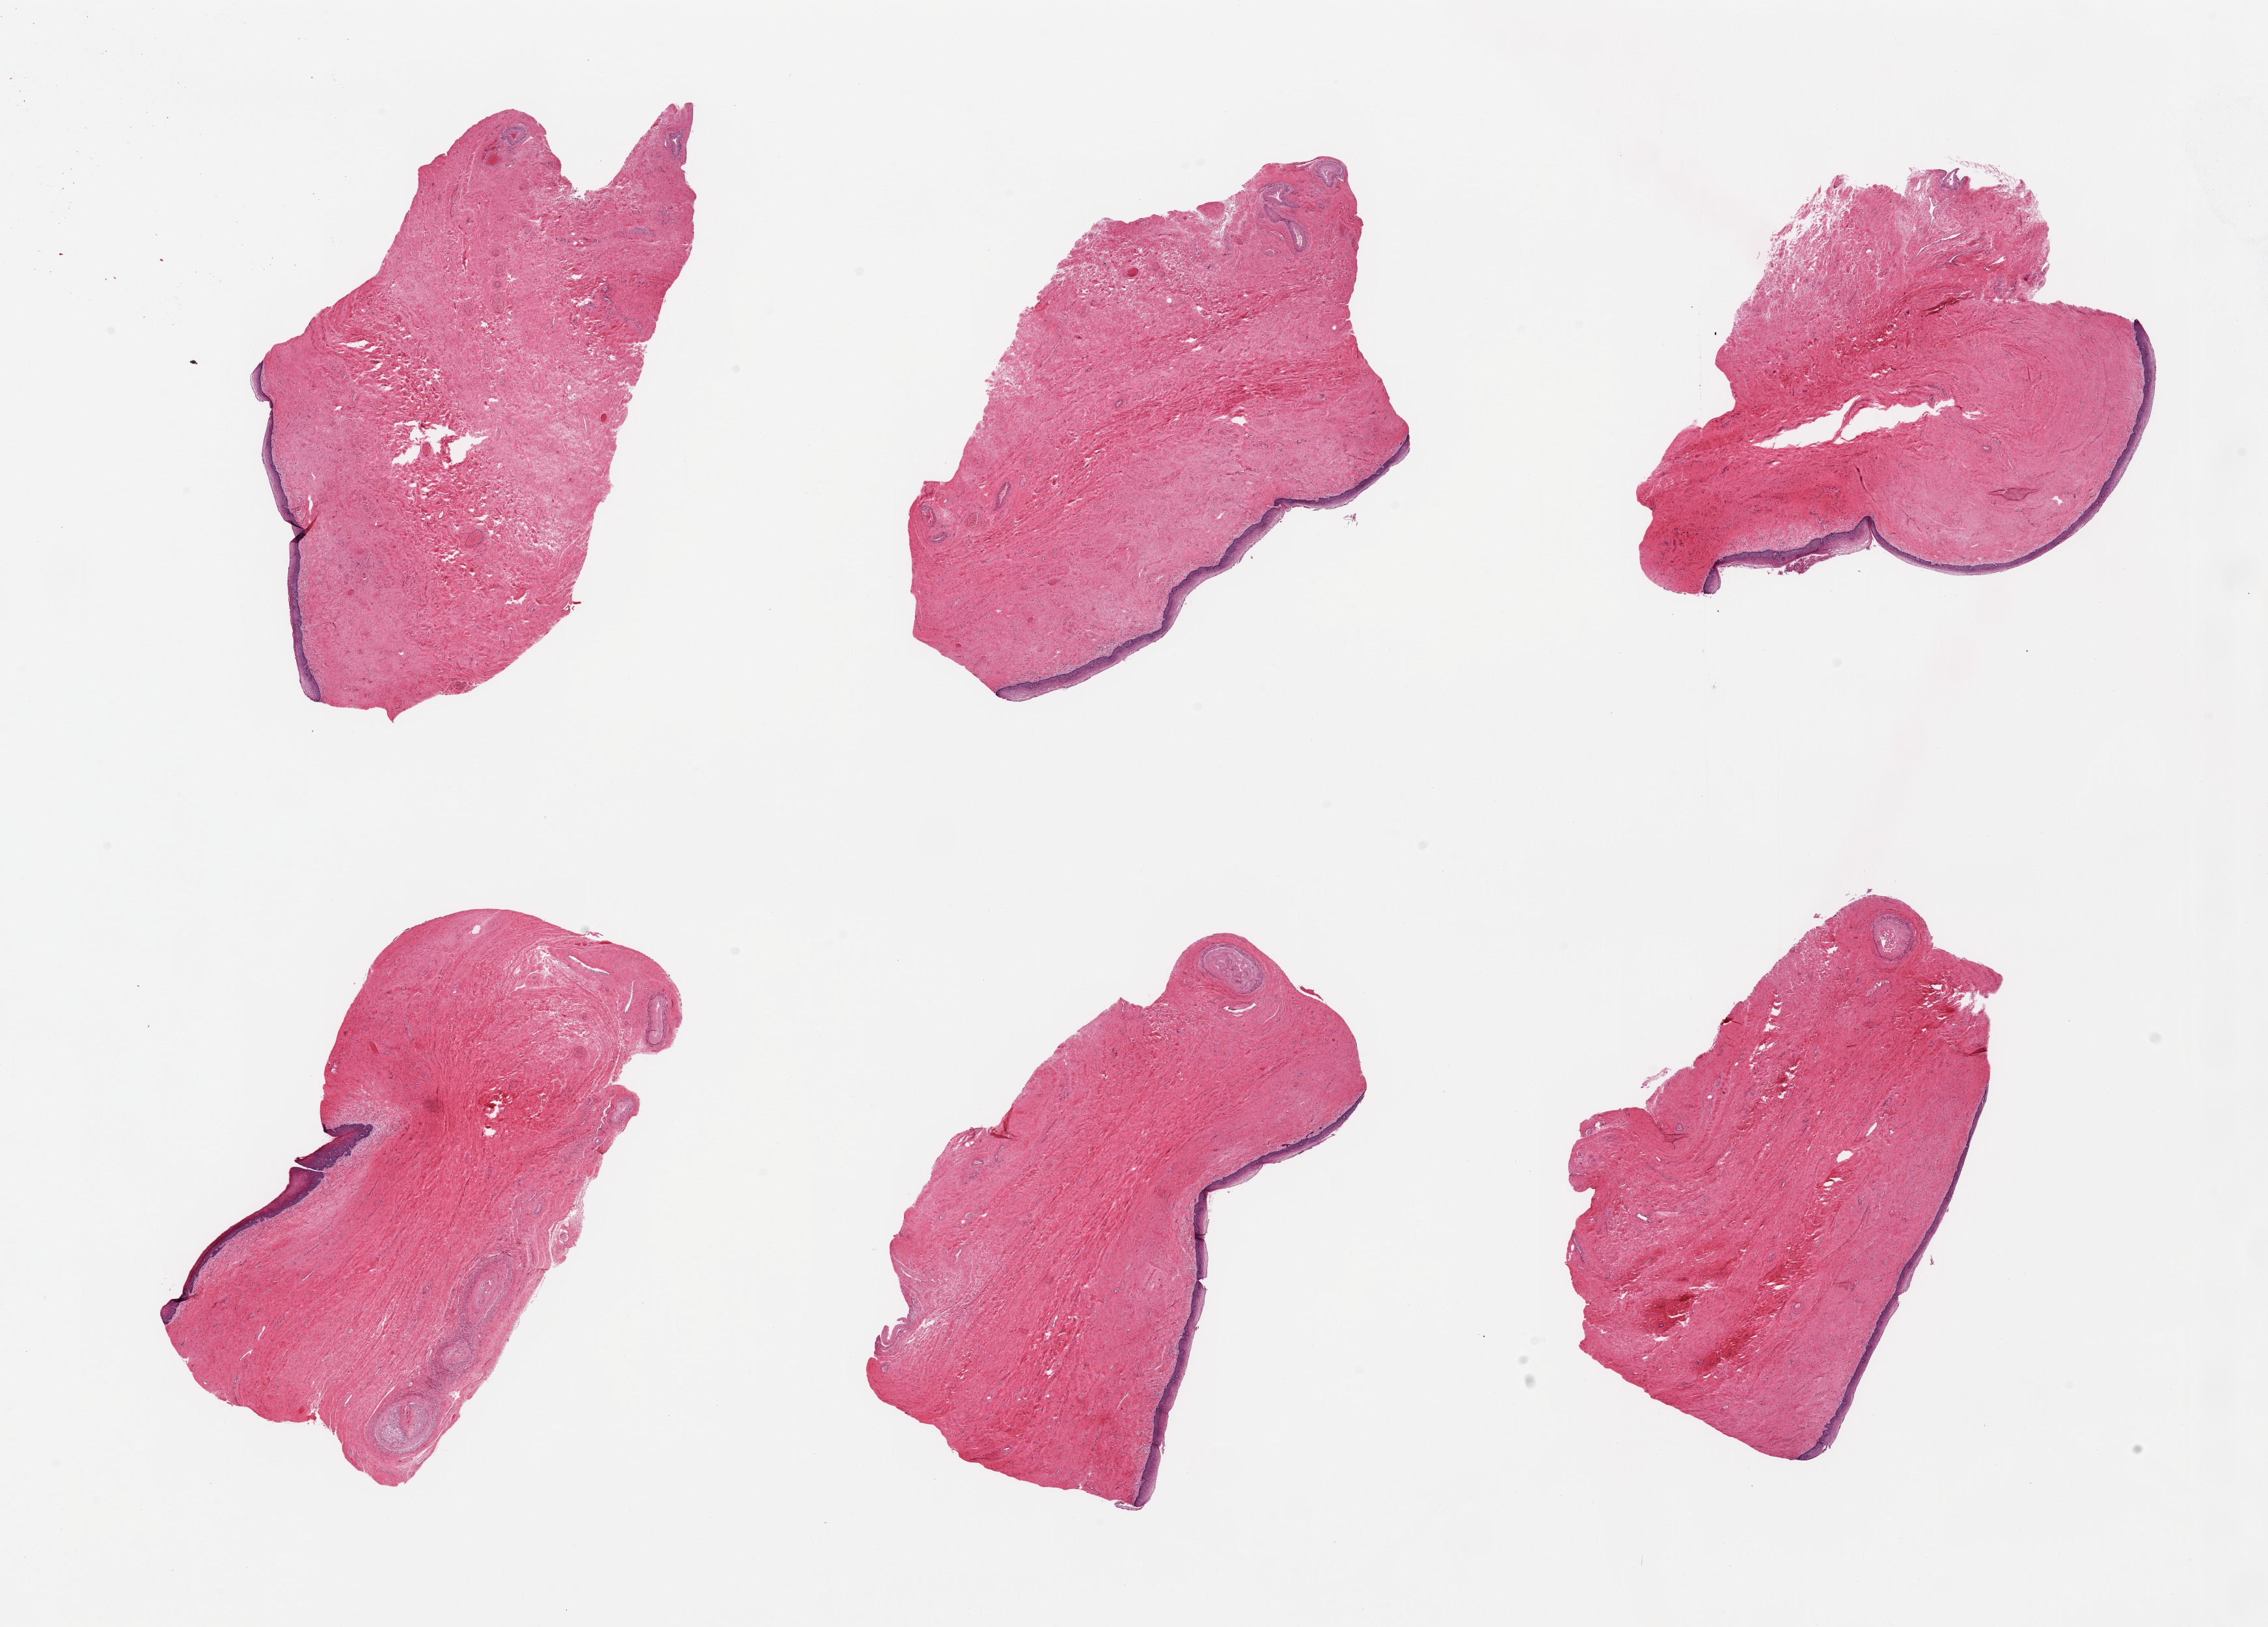
Digitized H&E-stained section, whole scanned area (about 27.6 x 19.8 mm) shown as a low-resolution overview; PAXgene-fixed, paraffin-embedded tissue; sampled site (target tissue): vagina; donor tissue sample. Donor sex: female.
Review note (as recorded): 6 pieces; preserved epithelium.